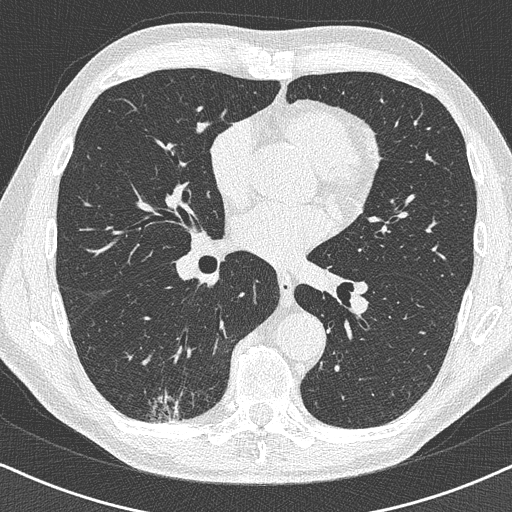
Chest CT (low-dose screening protocol), one axial image; first (baseline) screen; lung window (W 1500 / L -600 HU); lung (sharp) reconstruction kernel (B50f); 120 kVp; 512 × 512 image matrix, field of view 320 × 320 mm. Male participant, aged 63 years at enrolment. Former smoker at enrolment.
- Lesion marked by an expert reader, box from (x=129, y=360) to (x=201, y=428) px.
- Reader record for this screening exam (exam-level; its link to the box is not recorded): non-calcified nodule or mass ≥4 mm, right lower lobe, 16 × 13 mm, poorly defined margins.
- Later outcome: lung cancer diagnosed 74 days after this screen — adenocarcinoma, NOS, right lower lobe, moderately differentiated (G2), stage IA (AJCC 6th edition), 20 mm at pathology.